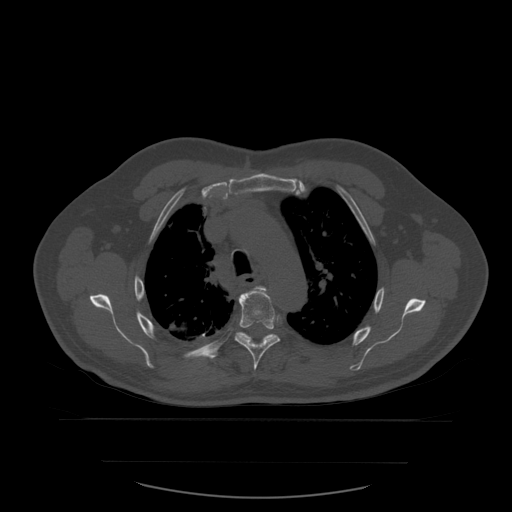
CT including the spine, one axial slice; slice 423 of 590 in the series (ordered by position); bone window (W 1800 / L 400 HU); 1.25 mm slice thickness; 512 × 512 image matrix, field of view 479 × 479 mm. Patient age 71 years. Case-level facts recorded for this patient, not image findings: primary cancer: lung.
Annotated regions visible in this slice (semi-automatically segmented with operator editing):
- T4 vertebra: bounding box (x1, y1, x2, y2) in pixels: (253, 287, 267, 291)
- T5 vertebra: (234, 289, 280, 371)
- T6 vertebra: (241, 332, 274, 341)